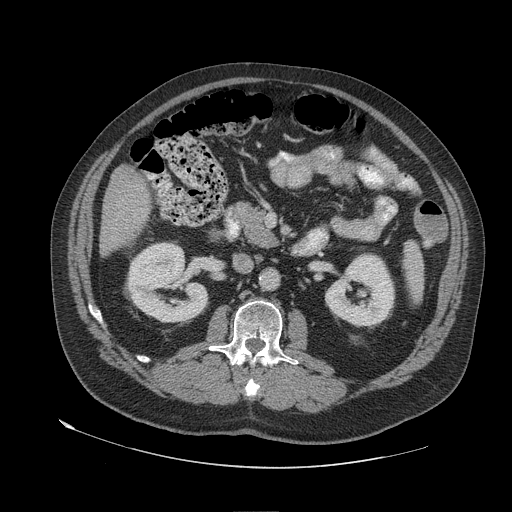
Contrast-enhanced abdominal CT (liver protocol), one axial slice. Slice 17 of 79 in the series (ordered by position). 140 kVp. Soft-tissue window (W 400 / L 40 HU). 2.5 mm slice thickness. 512 × 512 image matrix, field of view 480 × 480 mm. Case-level facts recorded for this patient, not image findings: diagnosis: hepatocellular carcinoma (patient treated with transarterial chemoembolisation; whether this scan precedes or follows treatment is not stated here); TNM stage (as recorded): Stage-IVA; Child-Pugh class: A; tumour differentiation: well differentiated.
Outlined on this slice (semi-automatically segmented with operator editing):
- liver parenchyma outside the tumour (the mass and vessels are separate outlines, so this box may not span the whole liver): bounding box [x1, y1, x2, y2] px = [100, 166, 150, 256]